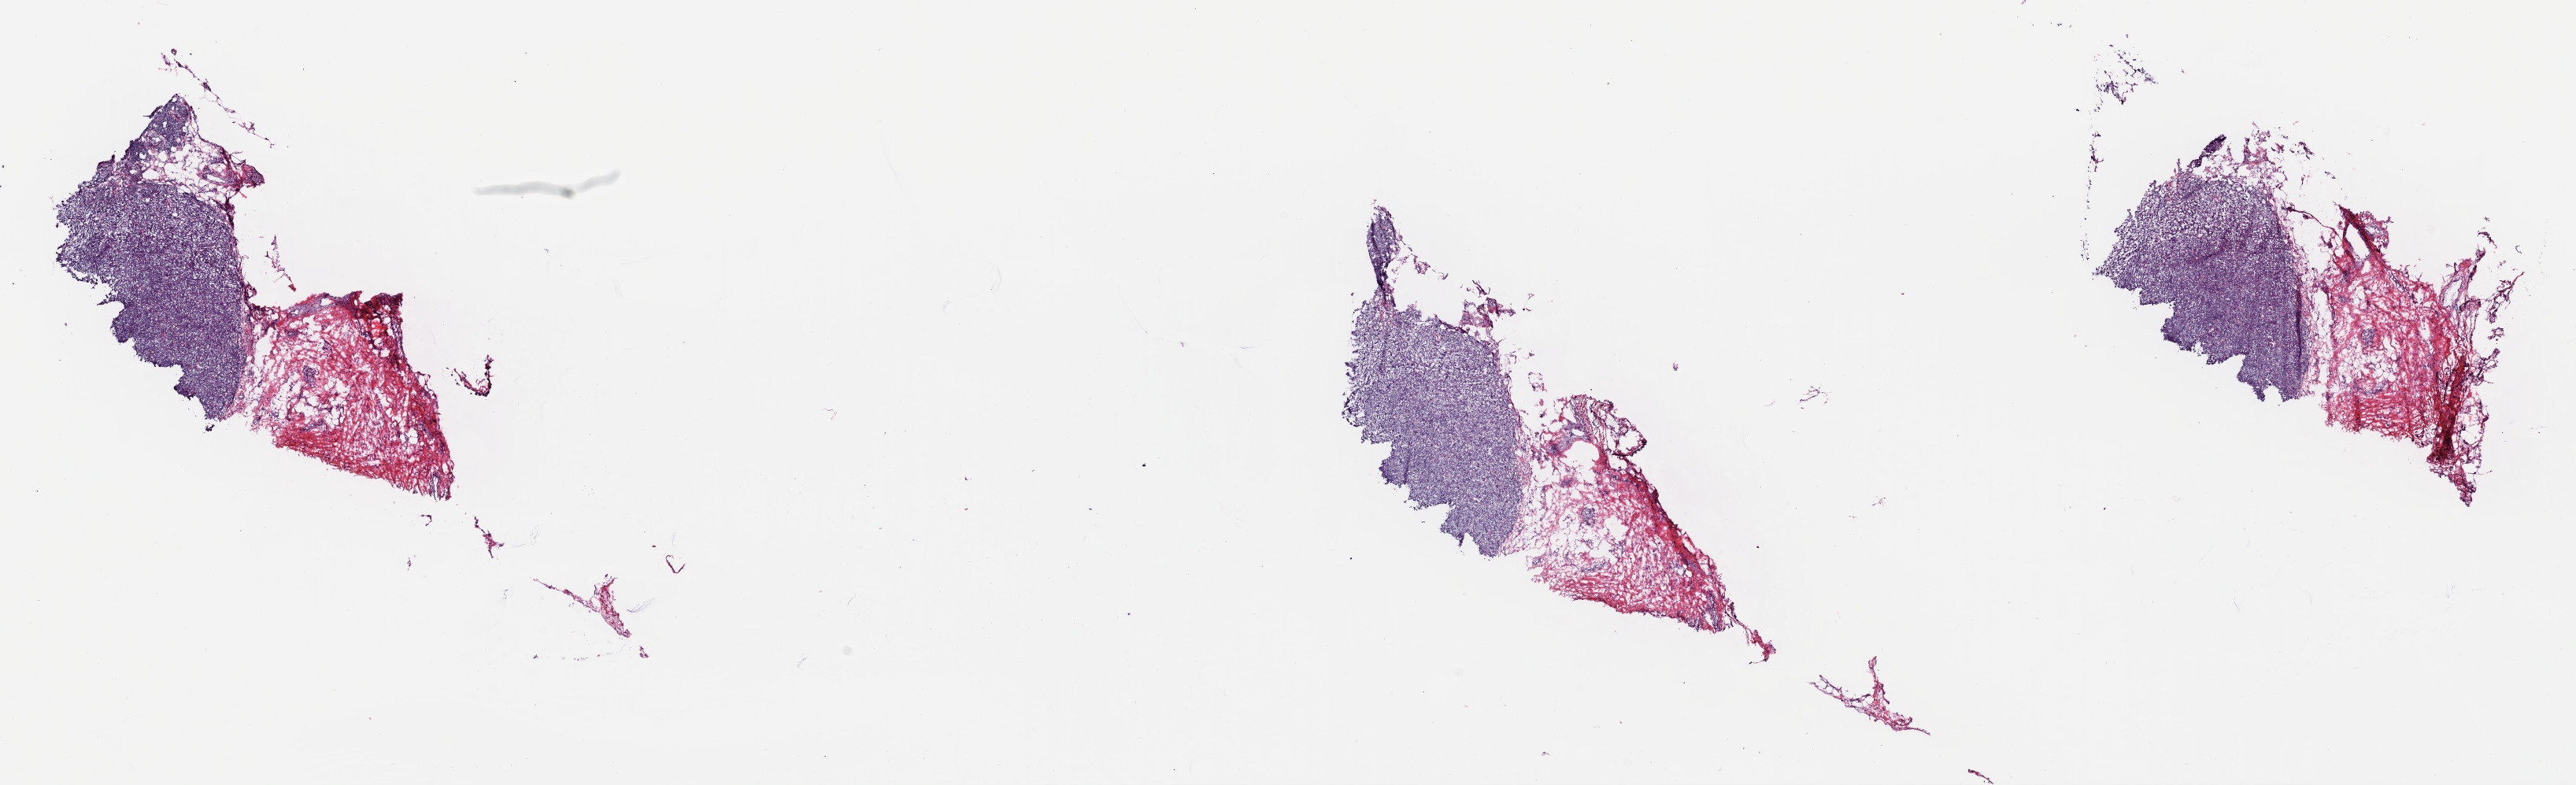
Digitized Hematoxylin and eosin (H&E) stained tissue section (whole slide), shown as a low-resolution overview of the whole scanned area (about 25.8 x 7.9 mm), frozen section, metastatic tumour sample, sampled site: lymph nodes of axilla or arm. Male, age 51 years at initial diagnosis. Pathologist review of this section (percent, as recorded): tumour cells 70%, tumour nuclei 70%, normal cells 0%, stromal cells 30%, necrosis 0%. Infiltration values recorded for this section: lymphocyte infiltration 8%, monocyte infiltration 1%, neutrophil infiltration 2%.
This section: metastatic tumour tissue. Patient diagnosis: Malignant melanoma, NOS.